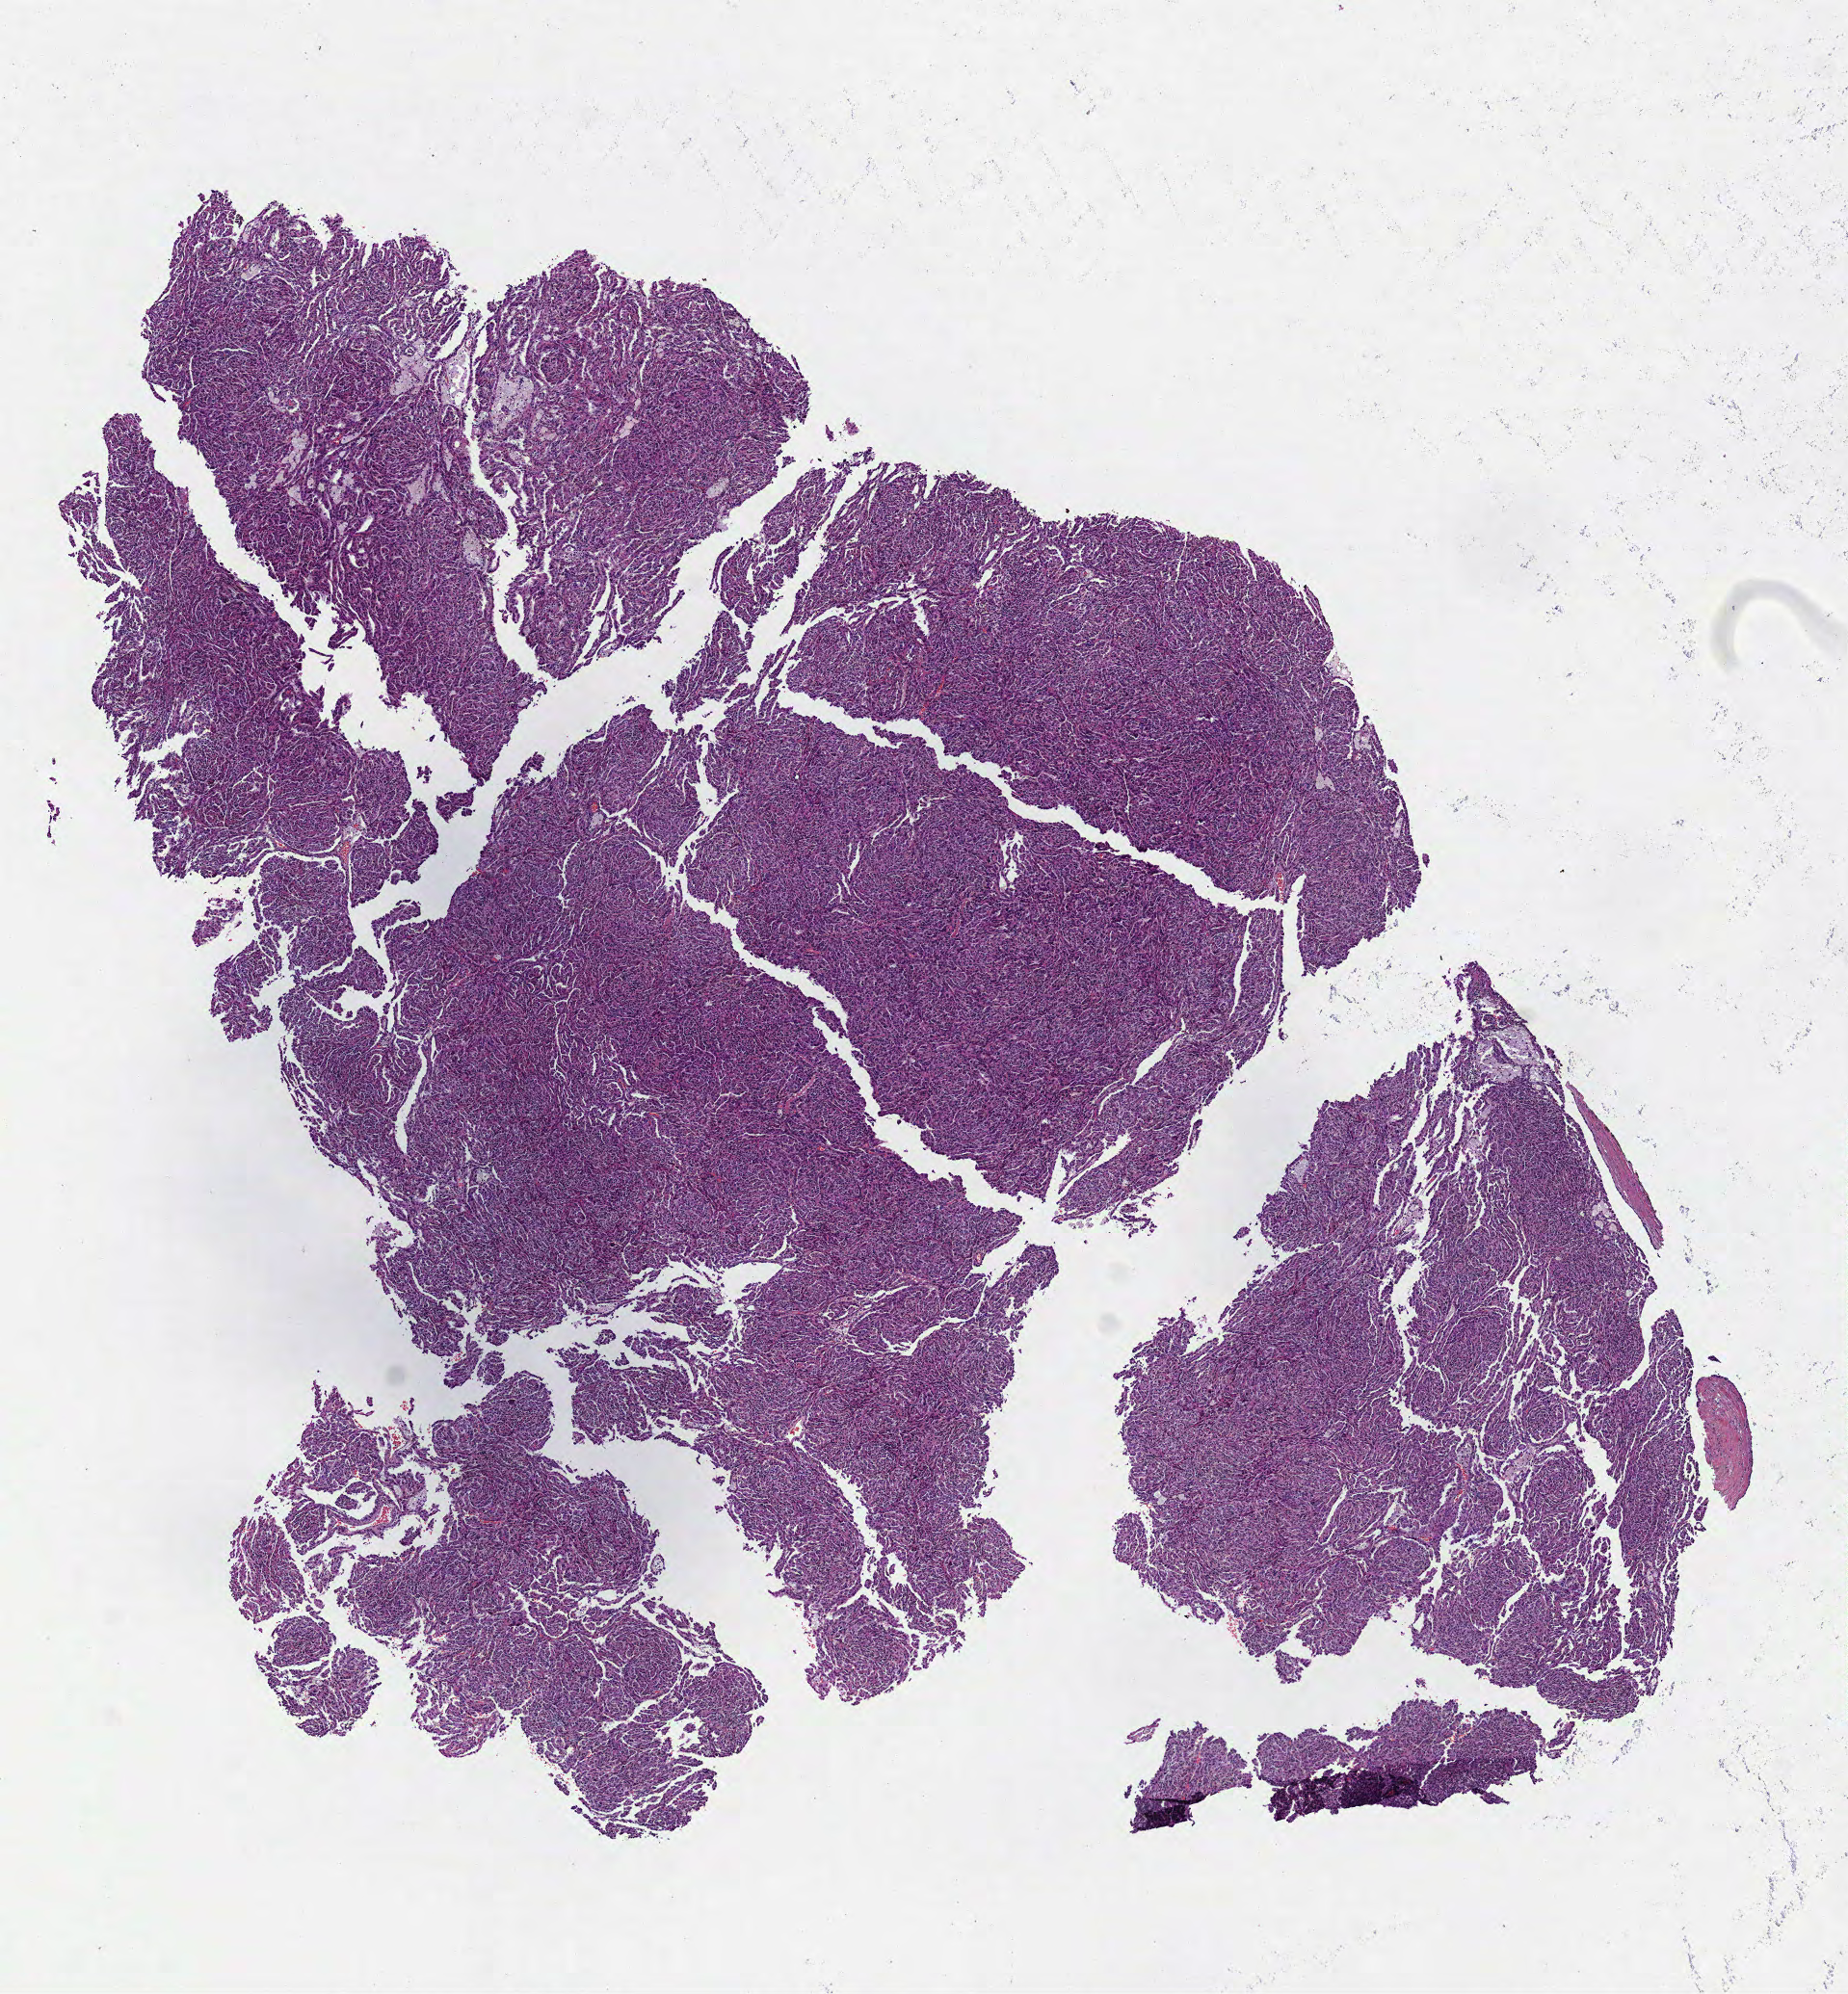
H&E whole-slide image — a low-resolution overview of the entire scanned area, about 7.7 x 8.3 mm; FFPE section; kidney, primary tumour sample. Male patient; age at initial diagnosis 60 years.
Diagnosis: Papillary adenocarcinoma, NOS.